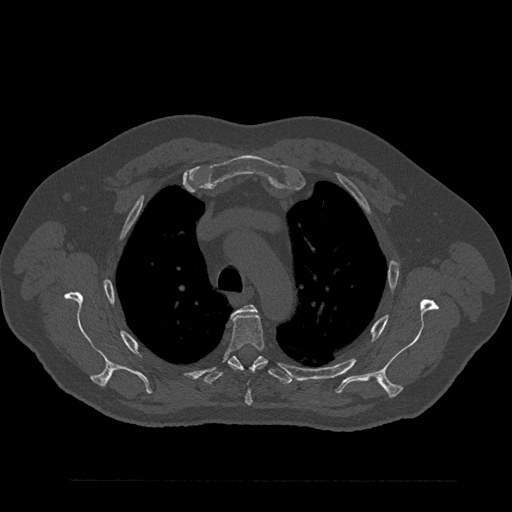
CT including the spine, one axial slice. Position 631 of 797 along the scan axis. Reconstruction kernel Br40s/3. 120 kVp. Bone window (W 1800 / L 400 HU). 0.5 mm slice thickness. 512 × 512 image matrix. Patient: male, 61 years. Case-level facts recorded for this patient, not image findings: primary cancer: prostate.
Annotated regions visible in this slice (semi-automatic segmentation, software-assisted and operator-edited):
- T3 vertebra: bounding box (x1, y1, x2, y2) in pixels: (233, 304, 257, 314)
- T4 vertebra: (228, 311, 265, 406)
- T5 vertebra: (204, 356, 292, 385)